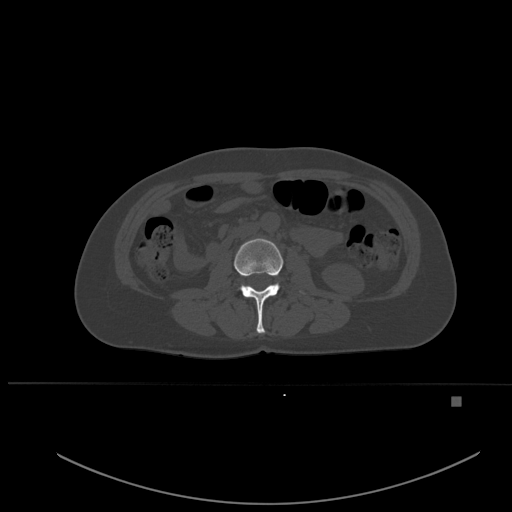
CT including the spine, one axial slice; slice 210 of 651 in the series (ordered by position); bone window (W 1800 / L 400 HU); 1.5 mm slice thickness; 512 × 512 image matrix. Female patient, age 49 years. From the clinical record (not read from this slice): primary cancer: breast.
Outlined on this slice (semi-automatic segmentation, software-assisted and operator-edited):
- L2 vertebra: bounding box (x1, y1, x2, y2) in pixels: (234, 238, 304, 333)